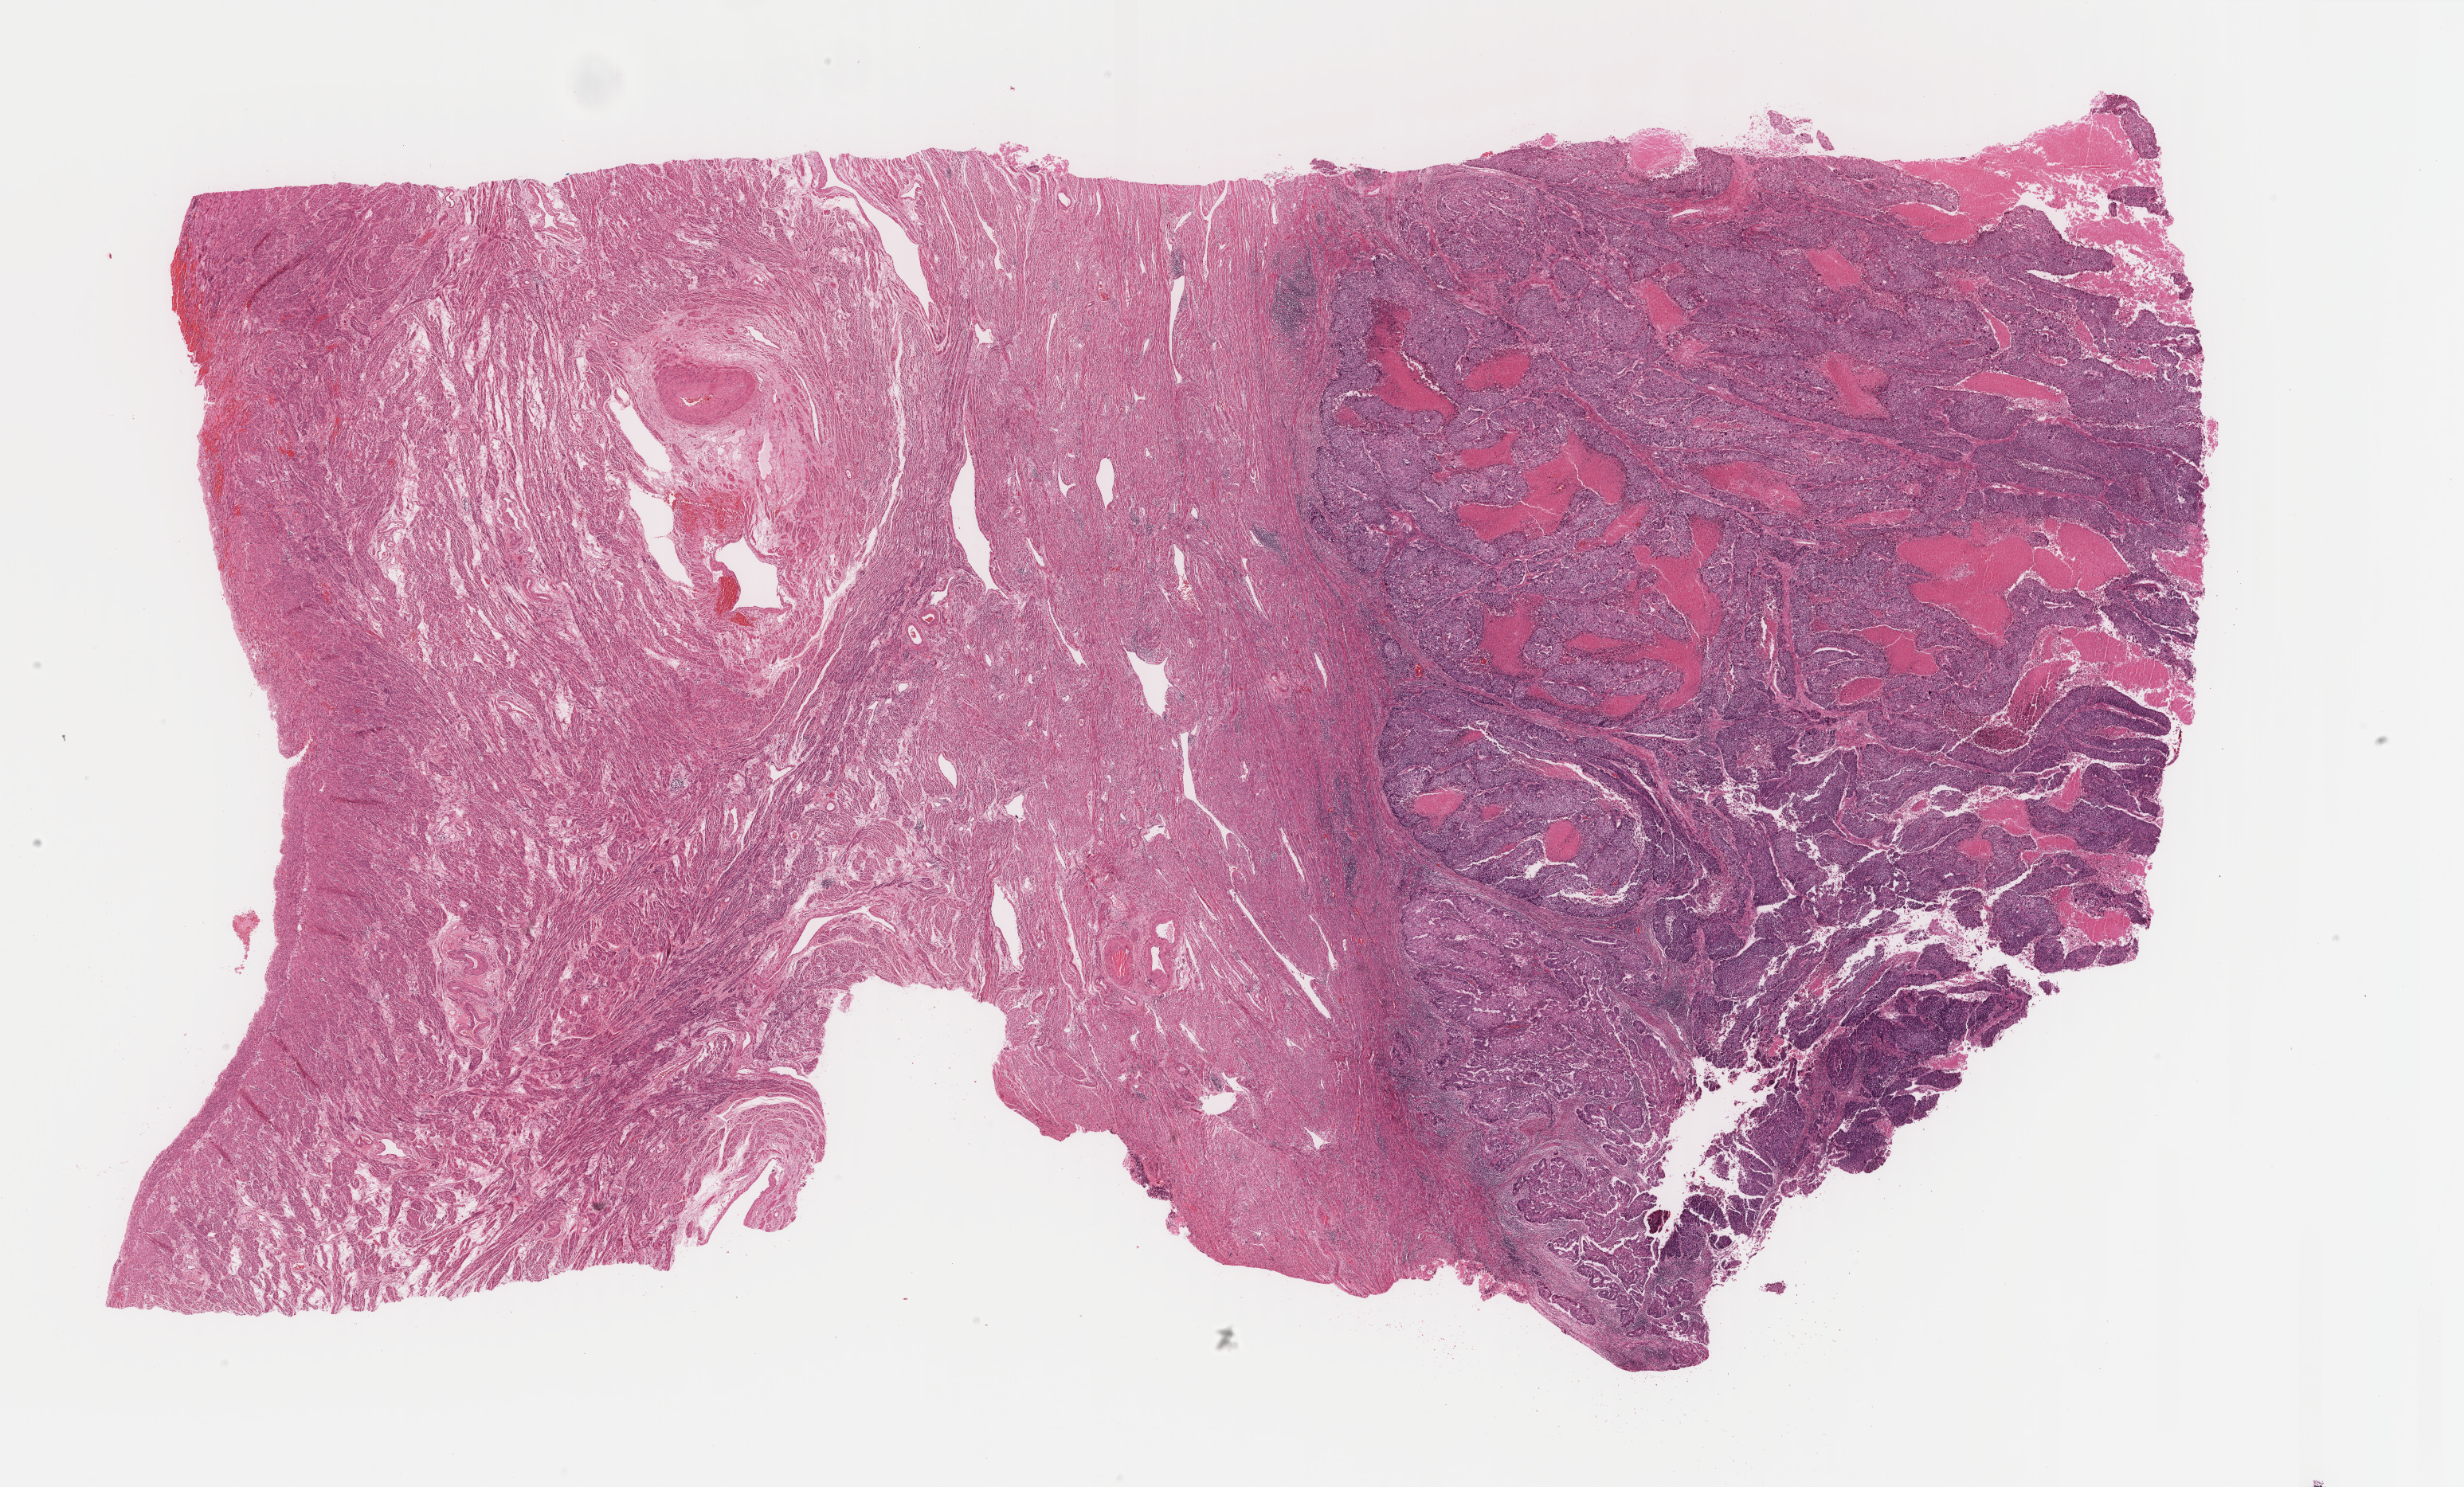
H&E-stained whole-slide image — shown as a low-resolution overview of the whole scanned area (about 24.6 x 14.8 mm, acquisition: 40x scan), formalin-fixed paraffin-embedded (FFPE) diagnostic section, primary tumour sample from the uterus. Female patient; age at initial diagnosis 60 years. Histologic grade: G3 (poorly differentiated).
* diagnosis: Endometrioid adenocarcinoma, NOS
* FIGO stage: IB